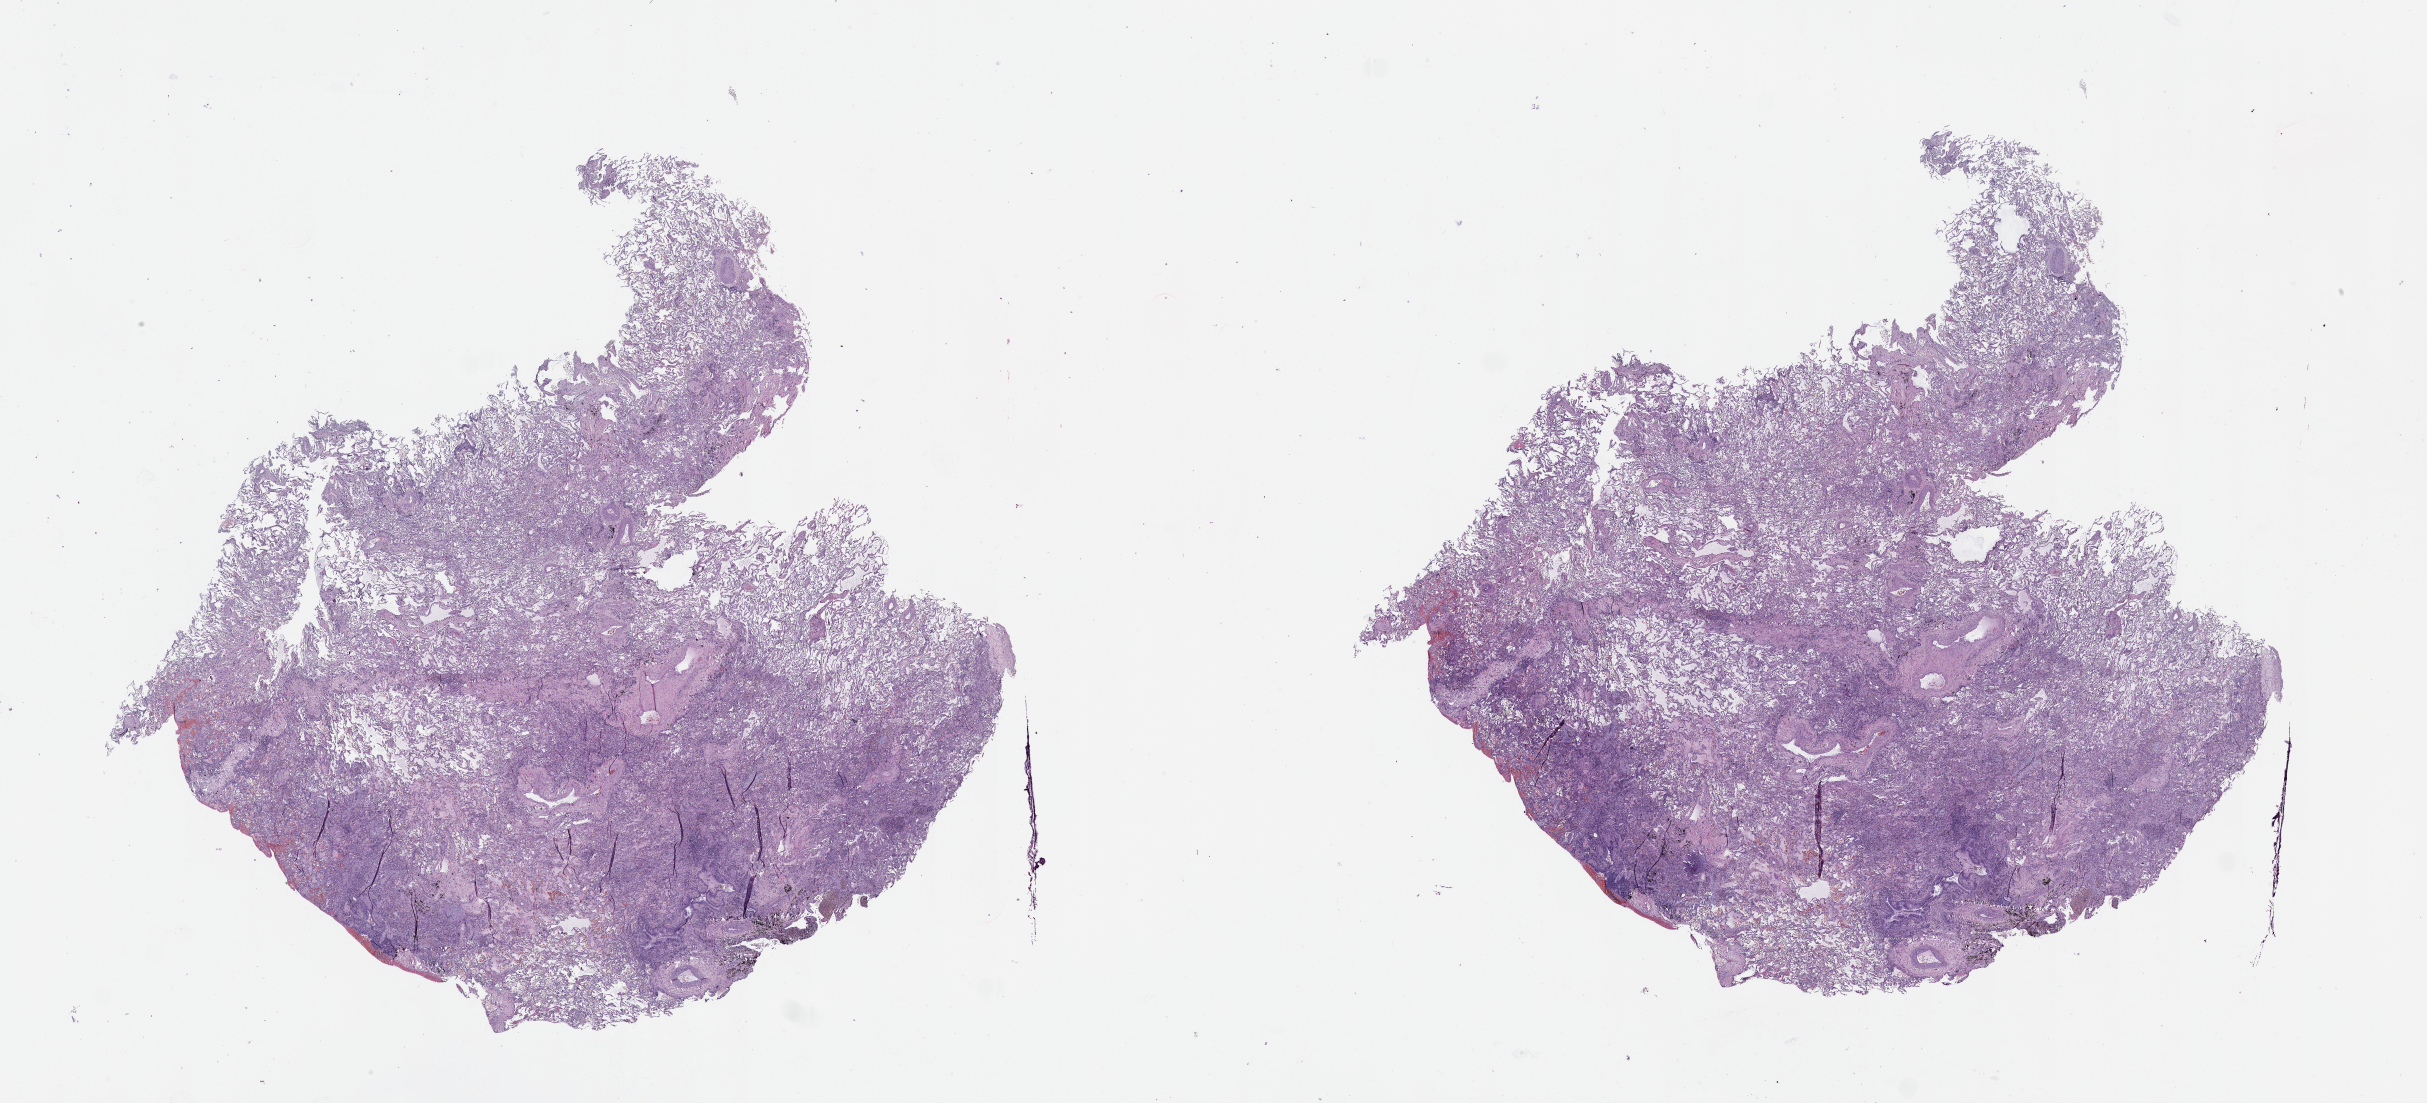
Whole-slide histology image, H&E — shown as a low-resolution overview of the whole scanned area (about 39.1 x 17.8 mm); lung, normal (non-tumour) tissue. Male, 57 y/o.
• this section: normal (non-tumour) tissue from the same patient
• patient diagnosis (cohort enrolment): squamous cell carcinoma (lung)